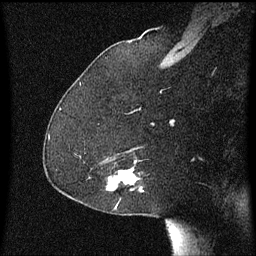
Breast MRI (dynamic contrast-enhanced), one sagittal slice; position 41 of 60 along the scan axis; dynamic contrast-enhanced series, image 2 of 3 at this slice position (ordered by acquisition); 1.5 T; TE 4.2 ms, TR 8.4 ms; 2 mm slice thickness; 256 × 256 image matrix, field of view 200 × 200 mm. Patient: female, 59 years.
Structures marked on this image (semi-automatically segmented with operator editing):
- analysis volume of interest (the breast-tissue region the enhancement analysis was run in; not a lesion): bounding box (x1, y1, x2, y2) in pixels: (106, 168, 143, 193)
- tumour enhancement mask (voxels above the 70 % enhancement threshold inside the analysis volume of interest): (116, 170, 135, 179)